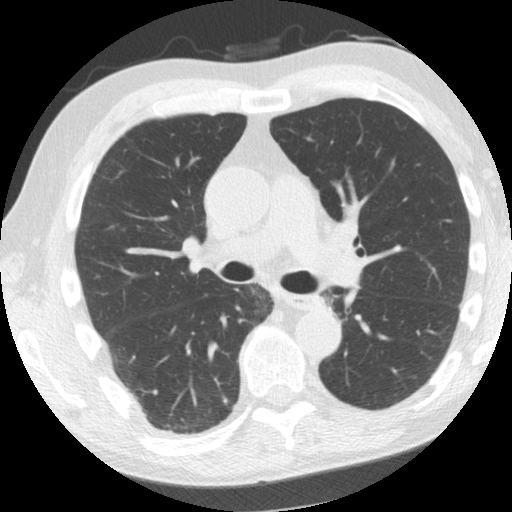
Low-dose screening chest CT, axial slice, second screening round (one year after baseline), lung window (W 1500 / L -600 HU), 2.5 mm slice thickness, standard (soft-tissue) reconstruction kernel (STANDARD), 120 kVp, 512 × 512 image matrix, field of view 324 × 324 mm. Male, age 61 years at enrolment. Former smoker at enrolment.
Expert-annotated lung lesion, bounding box [x1, y1, x2, y2] px = [307, 285, 350, 320]. Screening reader's record for this exam: no non-calcified nodule ≥4 mm recorded. Later outcome: lung cancer diagnosed 775 days after this screen (after the third annual screen) — squamous cell carcinoma, NOS, left upper lobe, left lower lobe, well differentiated (G1), stage IIB (AJCC 6th edition), 100 mm at pathology.